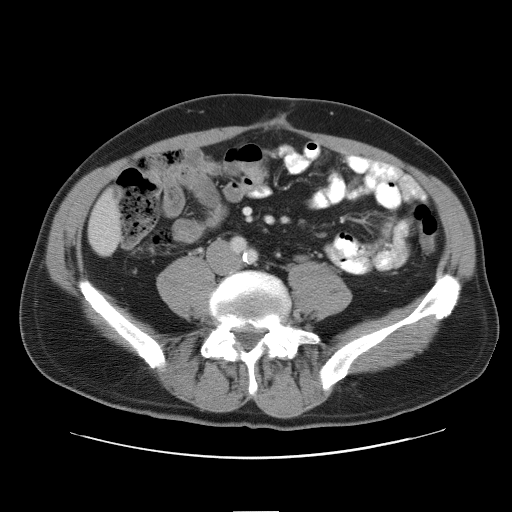
Contrast-enhanced abdominal CT, one axial slice; position 9 of 52 along the scan axis; reconstruction kernel STANDARD; 120 kVp; intravenous contrast given; soft-tissue window (W 400 / L 40 HU); 512 × 512 image matrix, field of view 393 × 393 mm. Male patient, age 70 years. Case-level facts recorded for this patient, not image findings: diagnosis: colorectal cancer liver metastases, imaged before liver resection; multiple liver metastases: yes; largest metastasis: 4 cm; disease in both lobes: yes.
Annotated regions visible in this slice (expert manual segmentation):
- liver: box from (x=89, y=193) to (x=121, y=256) px